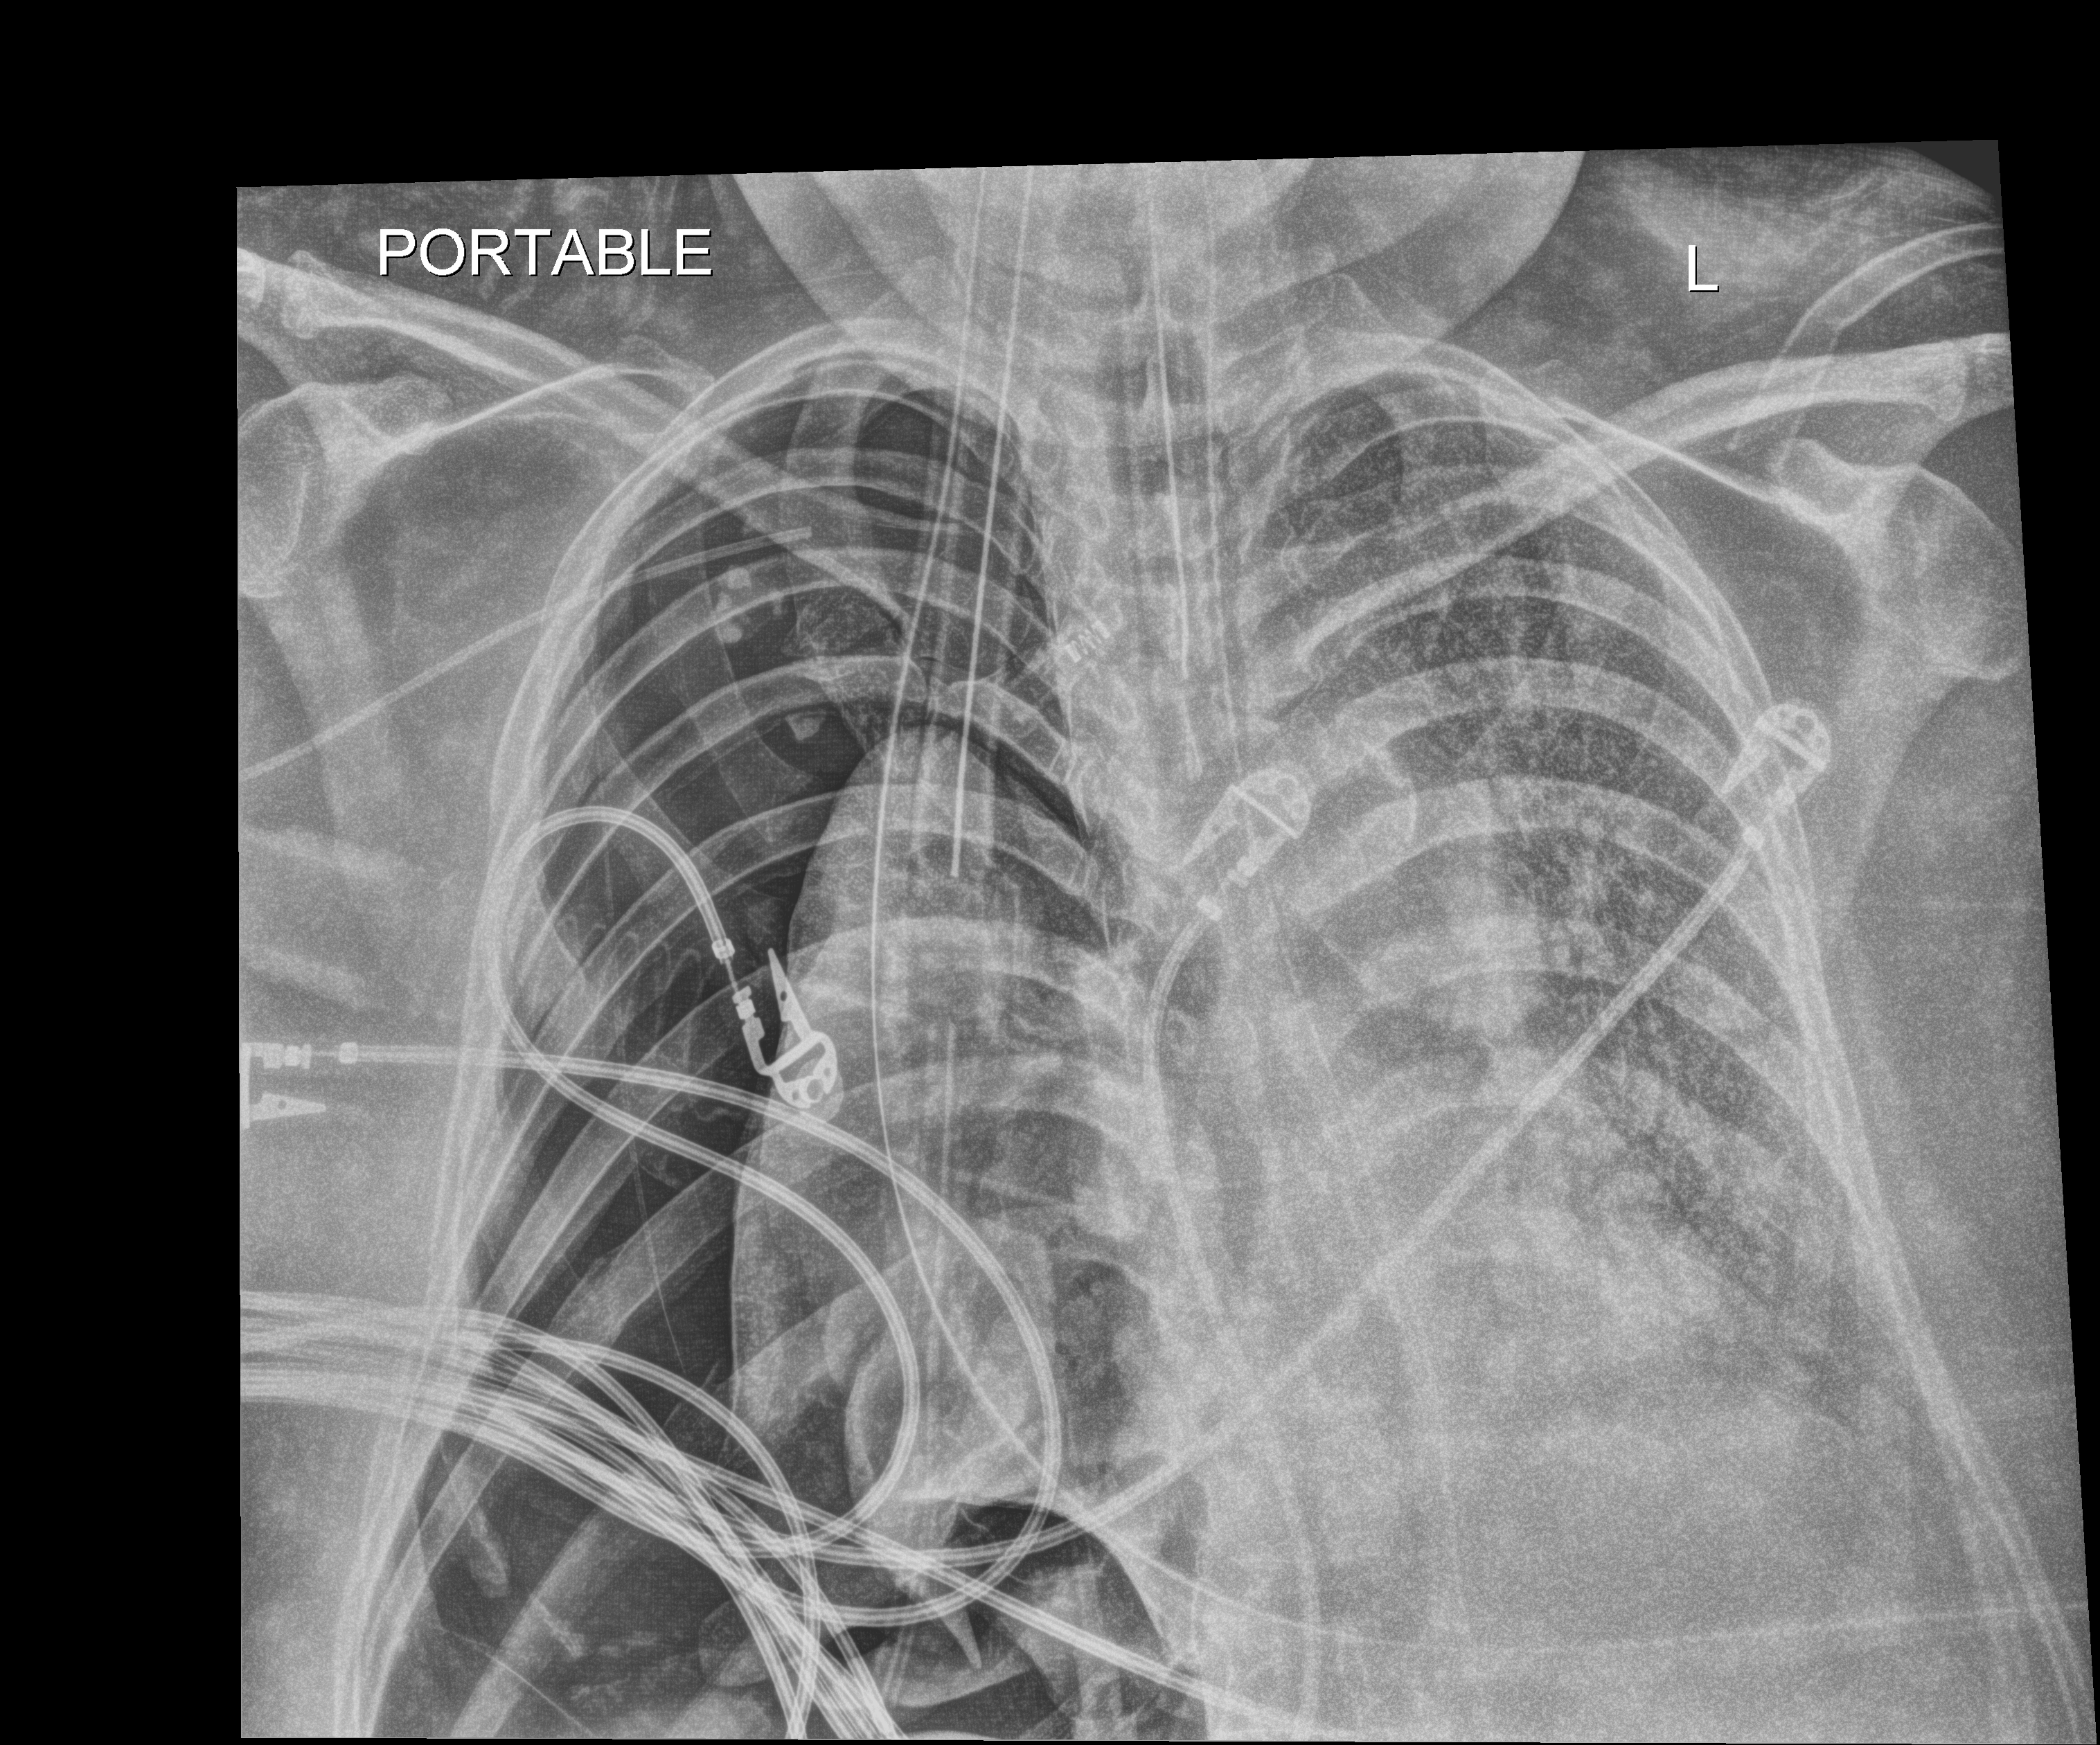
Chest X-ray (portable); anteroposterior (AP) projection. Patient hospitalised with COVID-19, aged 18–59 years.
Admission-level facts for this patient (not findings on this image; timing relative to this image not recorded): COPD (admission record): no; admitted to intensive care during this hospital stay: yes.